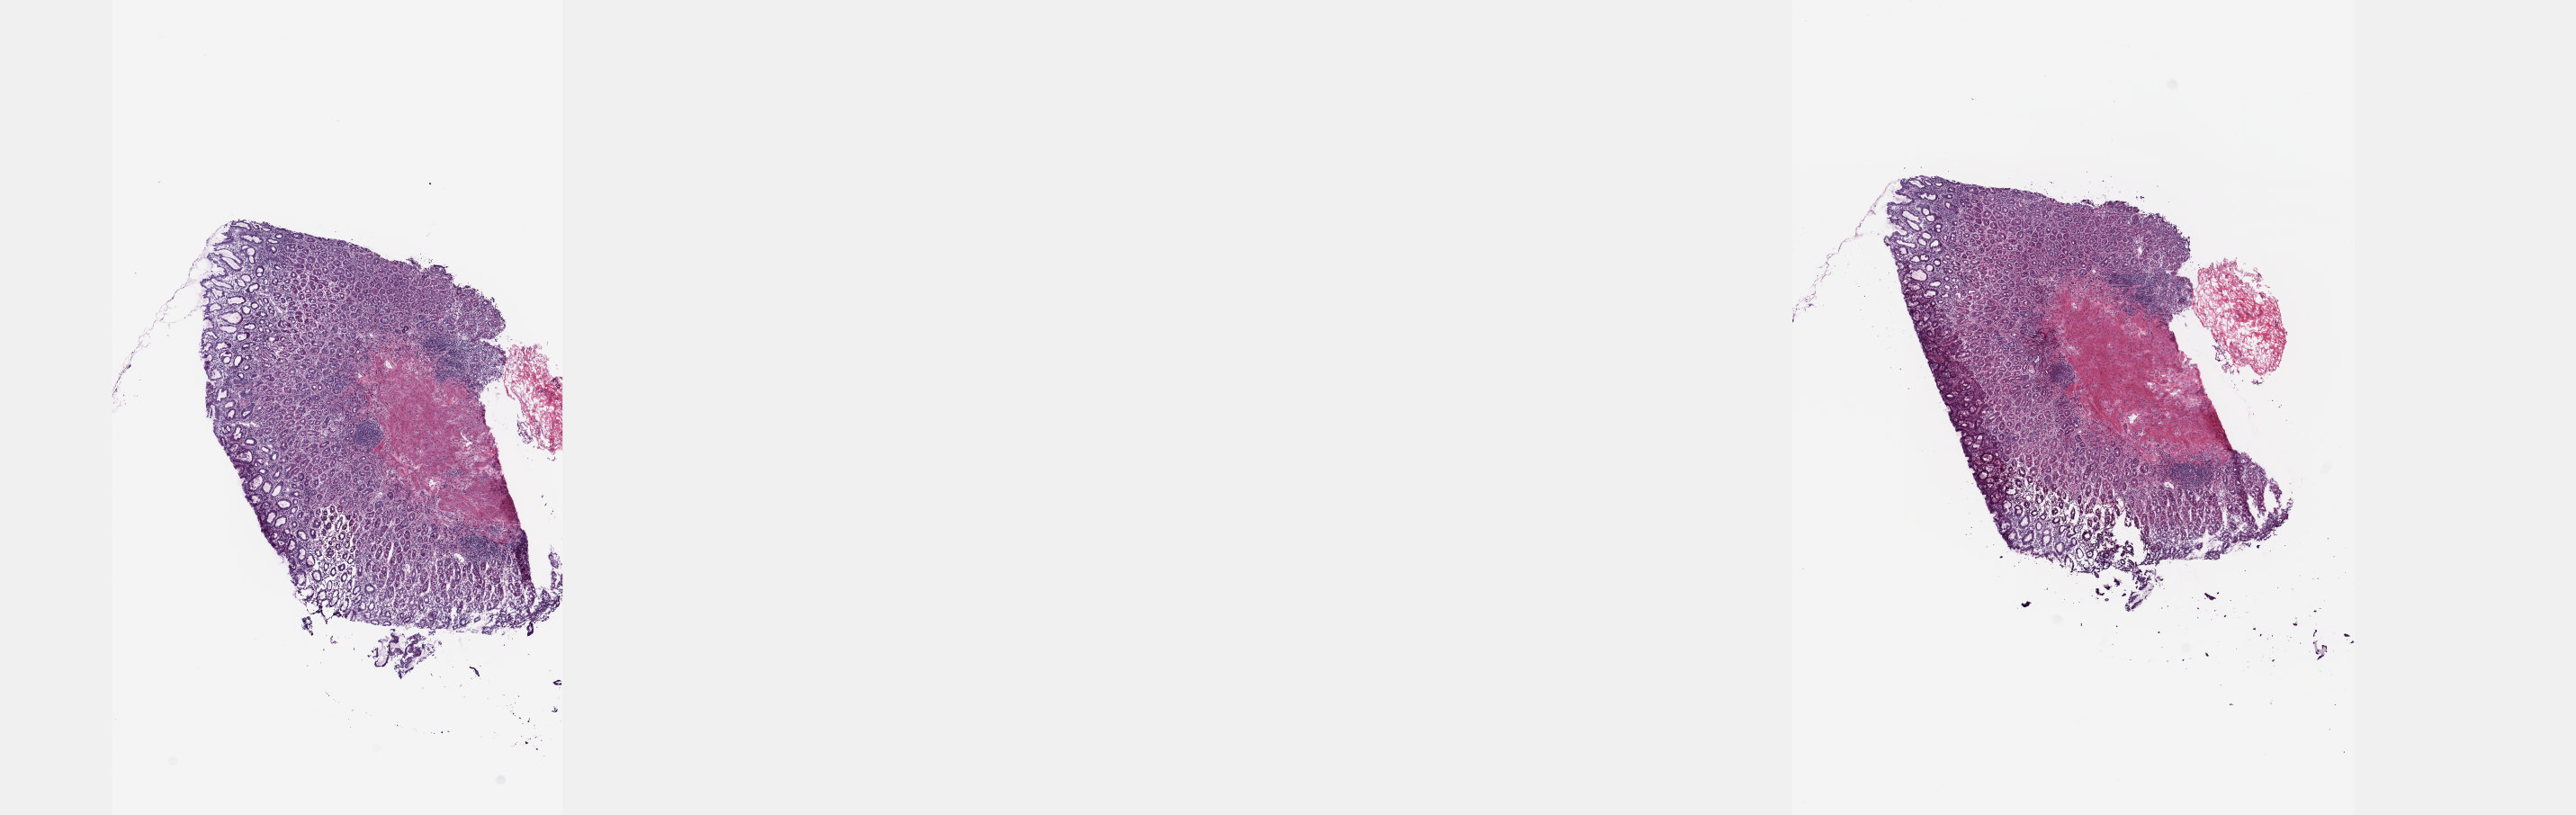
Whole-slide histology image, Hematoxylin and eosin (H&E) stained, low-resolution overview of the scanned area, about 23.1 x 7.3 mm (acquisition: 20x scan), frozen section, sample: solid tissue normal (non-tumour tissue), esophagus. Male, age 86 years at initial diagnosis.
This section: solid tissue normal sample (biorepository sample class). Patient diagnosis: Adenocarcinoma, NOS.